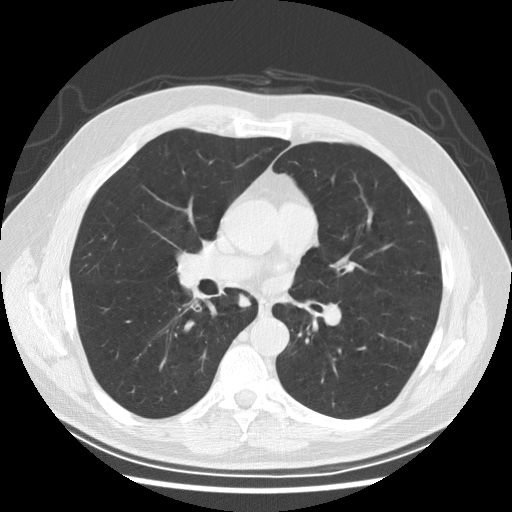
Axial slice from a low-dose chest CT screening exam, second screening round (one year after baseline), lung window (W 1500 / L -600 HU), 2.5 mm slice thickness, 120 kVp. Male participant, aged 61 years at enrolment. Former smoker at enrolment.
Expert reader's lesion annotation, box from (x=225, y=285) to (x=257, y=317) px. Screening reader's record for this exam: no non-calcified nodule ≥4 mm recorded. Official screen result: negative screen, minor abnormalities not suspicious for lung cancer. Participant outcome: lung cancer diagnosed 382 days after this screen — squamous cell carcinoma, keratinizing, NOS, right lower lobe, stage IIIB (AJCC 6th edition), 40 mm at pathology.